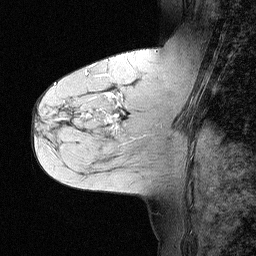
Breast MRI (dynamic contrast-enhanced), one sagittal slice. Dynamic contrast-enhanced study with each time point stored as its own series, time point 2 of 3 at this slice position (early post-contrast, ordered by acquisition time). 1.5 T. TE 4.5 ms, TR 11 ms. 2.06 mm slice thickness. 256 × 256 image matrix. Patient: female, 55 years. From the clinical record (not read from this slice): setting: breast cancer imaged before/during neoadjuvant chemotherapy; receptor status: triple-negative.
Outlined on this slice (semi-automatic segmentation, software-assisted and operator-edited):
- analysis volume of interest (the breast-tissue region the enhancement analysis was run in; not a lesion): bounding box <71,63,147,145> (left, top, right, bottom; pixels)
- tumour enhancement mask (voxels above the 90 % enhancement threshold inside the analysis volume of interest): <82,97,117,127>